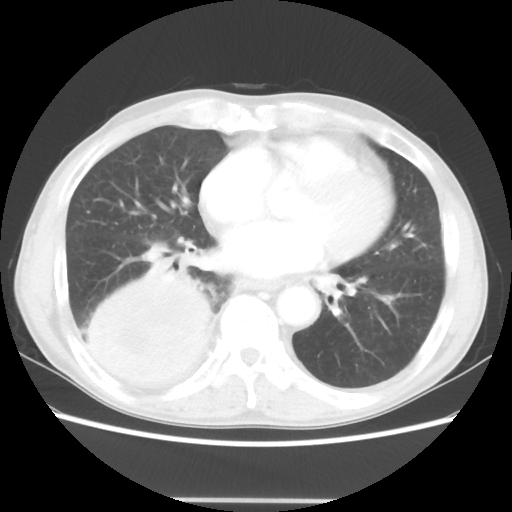
Chest CT, one axial slice; slice 17 of 48 in the series (ordered by position); 100 kVp; lung window (W 1500 / L -600 HU); 5 mm slice thickness; 512 × 512 image matrix, field of view 361 × 361 mm. Patient: male, 66 years. Case-level facts recorded for this patient, not image findings: clinical TNM (as recorded): T4 N1 M1; histopathological grade: G3.
Outlined on this slice (bounding box drawn by a radiologist):
- lung tumour (recorded histology: small cell carcinoma): bounding box (x1, y1, x2, y2) in pixels: (81, 272, 229, 395)